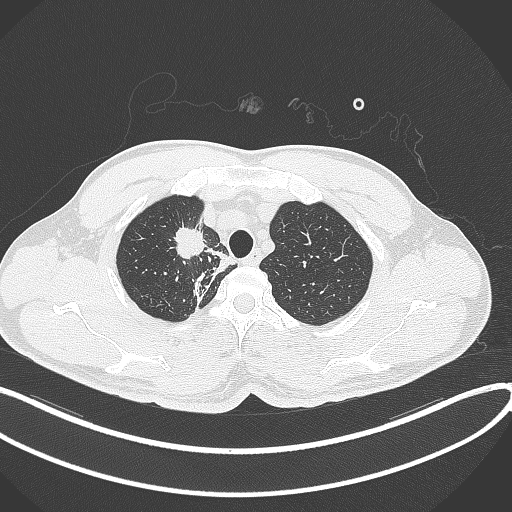
Chest CT, one axial slice; reconstruction kernel B70f; 120 kVp; lung window (W 1500 / L -600 HU); 1 mm slice thickness; 512 × 512 image matrix. Male patient, age 48 years. Case-level facts recorded for this patient, not image findings: clinical TNM (as recorded): T1c N1 M1.
Structures marked on this image (rectangle marked by the reading radiologist):
- lung tumour (recorded histology: adenocarcinoma): bounding box <168,228,205,265> (left, top, right, bottom; pixels)